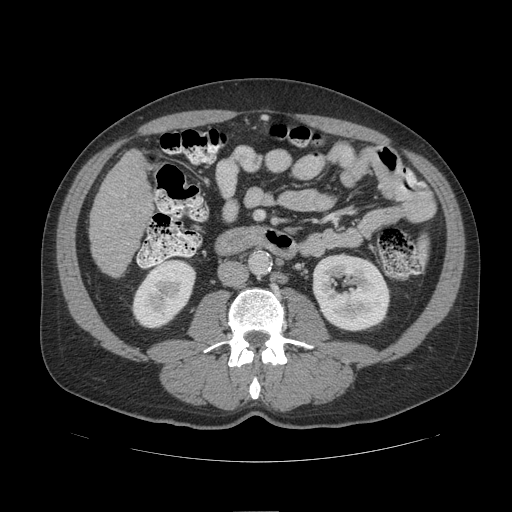
Contrast-enhanced abdominal CT (liver protocol), one axial slice. Position 32 of 109 along the scan axis. Reconstruction kernel STANDARD. 140 kVp. Soft-tissue window (W 400 / L 40 HU). 2.5 mm slice thickness. 512 × 512 image matrix, field of view 420 × 420 mm. From the clinical record (not read from this slice): diagnosis: hepatocellular carcinoma (patient treated with transarterial chemoembolisation; whether this scan precedes or follows treatment is not stated here); TNM stage (as recorded): Stage-IIIB; Child-Pugh class: A; tumour differentiation: poorly differentiated; tumour nodularity: multinodular.
Outlined on this slice (semi-automatically segmented with operator editing):
- liver parenchyma outside the tumour (the mass and vessels are separate outlines, so this box may not span the whole liver): bounding box (x1, y1, x2, y2) in pixels: (90, 150, 152, 276)